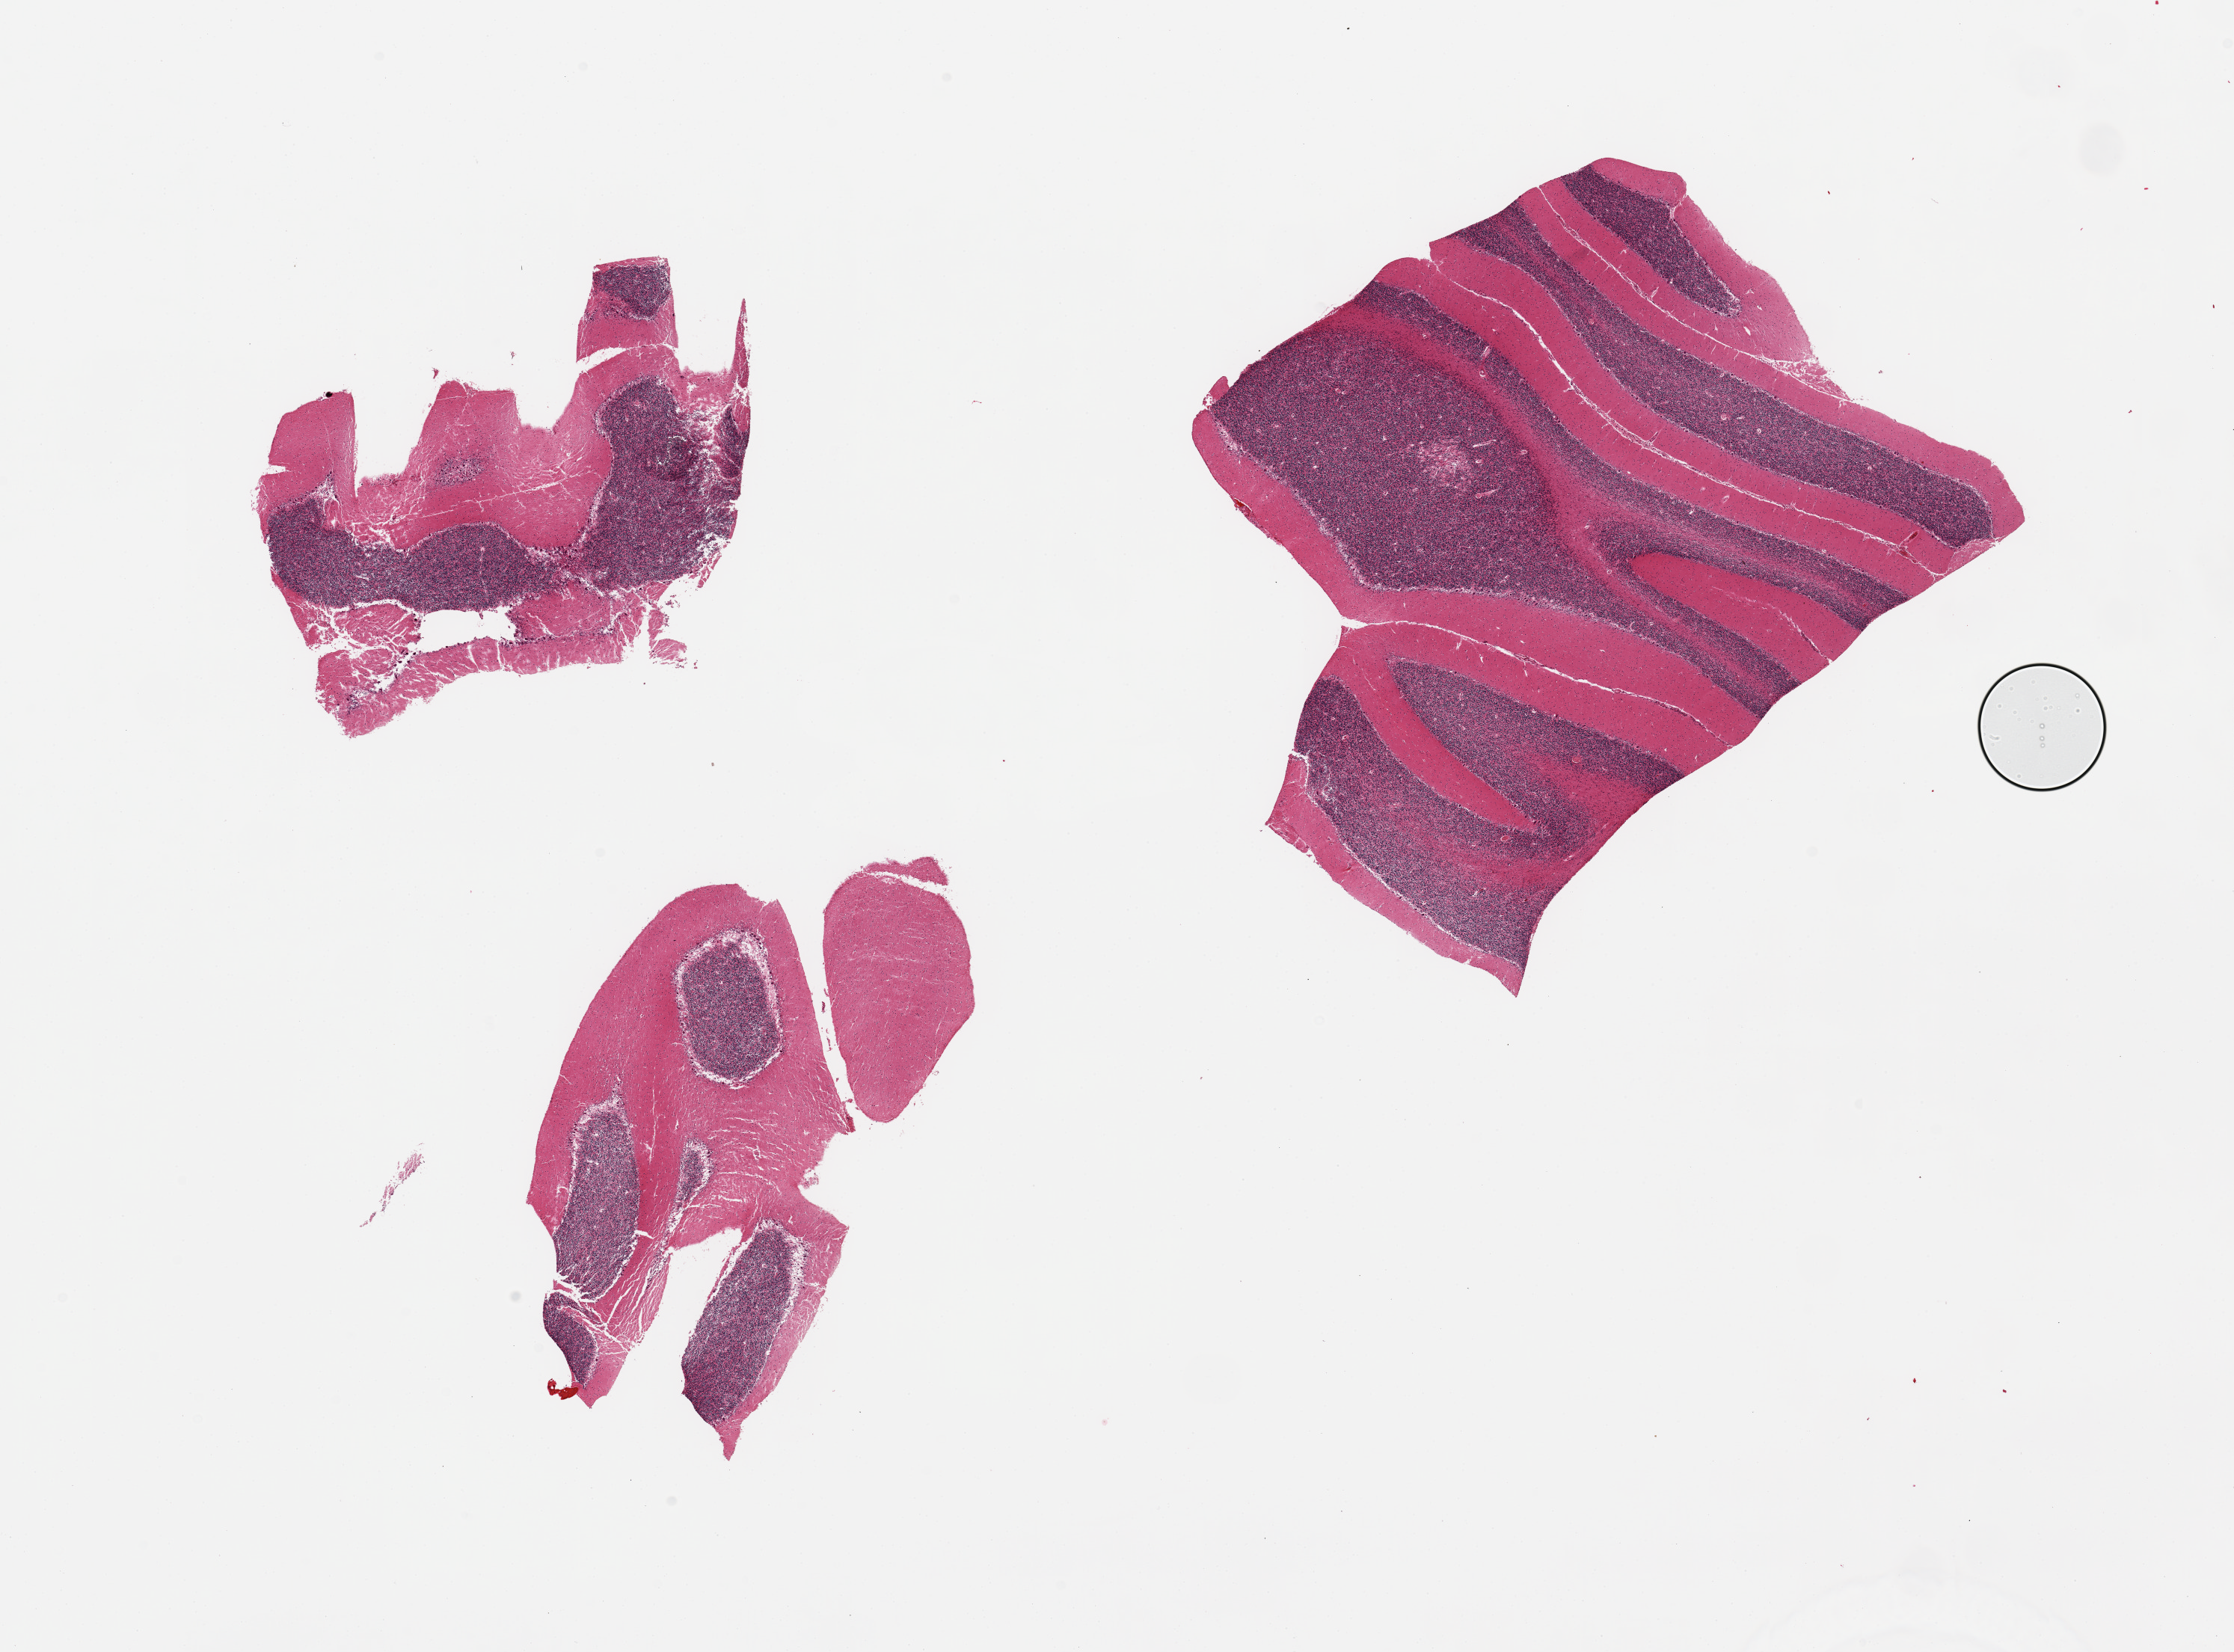
Whole-slide image, H&E stain — shown as a low-resolution overview of the whole scanned area (about 23.6 x 17.5 mm, slide scanned at 20x). PAXgene-fixed, paraffin-embedded tissue. Section of cerebellum (target tissue). Donor tissue sample.
Review note (as recorded): 3 pieces; mild to moderate autolysis, Purkinje cells well visualized with changes suggestive of hypoxic damage.